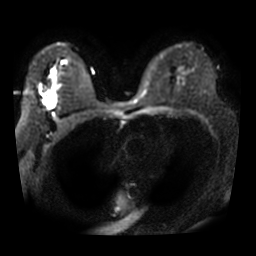
Breast MRI, one axial slice. Slice 21 of 32 in the series (ordered by position). Diffusion-weighted series; image 2 of 4 stored at this slice position (different b-values; order by instance number). 3 T. 256 × 256 image matrix, field of view 340 × 340 mm. Female patient.
Outlined on this slice (expert manual segmentation):
- tumour on diffusion-weighted imaging: bounding box [x1, y1, x2, y2] px = [49, 94, 55, 108]